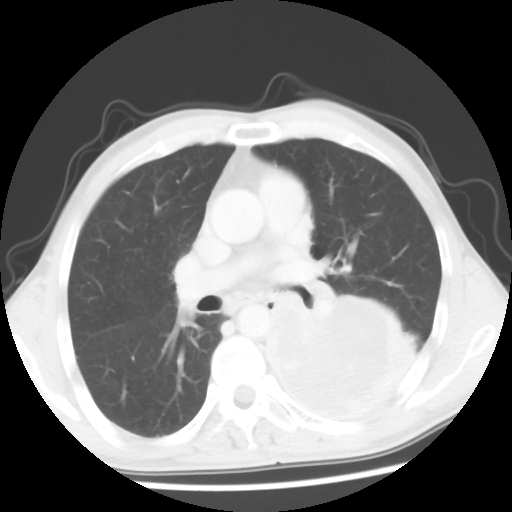
Chest CT, one axial slice; position 32 of 56 along the scan axis; reconstruction kernel STANDARD; lung window (W 1500 / L -600 HU); 5 mm slice thickness; 512 × 512 image matrix, field of view 318 × 318 mm. Patient: male, 60 years. From the clinical record (not read from this slice): clinical TNM (as recorded): T4 N0 M0.
Annotated regions visible in this slice (rectangle marked by the reading radiologist):
- lung tumour (recorded histology: squamous cell carcinoma): bounding box <261,277,420,425> (left, top, right, bottom; pixels)